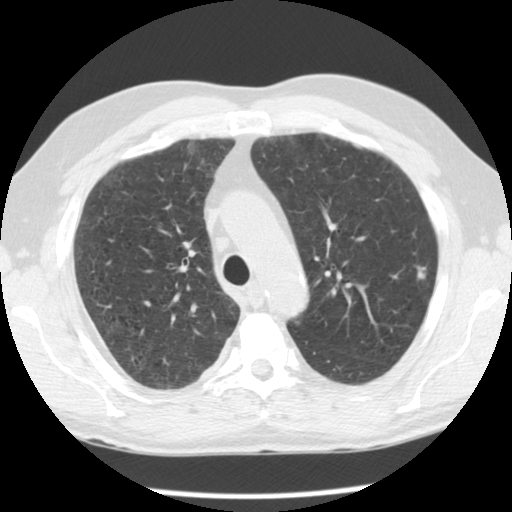
Chest CT (low-dose screening protocol), one axial image. Second screening round (one year after baseline). Lung window (W 1500 / L -600 HU). 2.5 mm slice thickness. 512 × 512 image matrix. Male participant, aged 59 years at enrolment. Current smoker at enrolment.
Expert-annotated lung lesion, box from (x=391, y=253) to (x=439, y=296) px. The screening reader recorded 2 non-calcified nodules or masses ≥4 mm on this exam (left upper lobe, right upper lobe); which of them this box marks is not recorded.